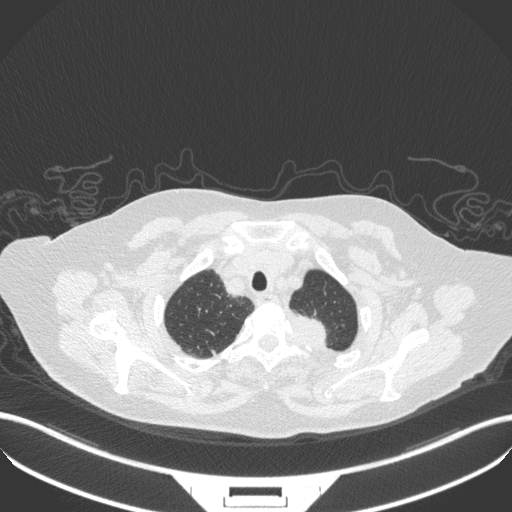
Chest CT, one axial slice; position 304 of 353 along the scan axis; reconstruction kernel B31f; lung window (W 1500 / L -600 HU); 1 mm slice thickness; 512 × 512 image matrix, field of view 400 × 400 mm. Female patient, age 81 years. Case-level facts recorded for this patient, not image findings: clinical TNM (as recorded): T2a N0 M0.
Annotated regions visible in this slice (rectangle marked by the reading radiologist):
- lung tumour (recorded histology: adenocarcinoma): bounding box (x1, y1, x2, y2) in pixels: (292, 308, 339, 352)